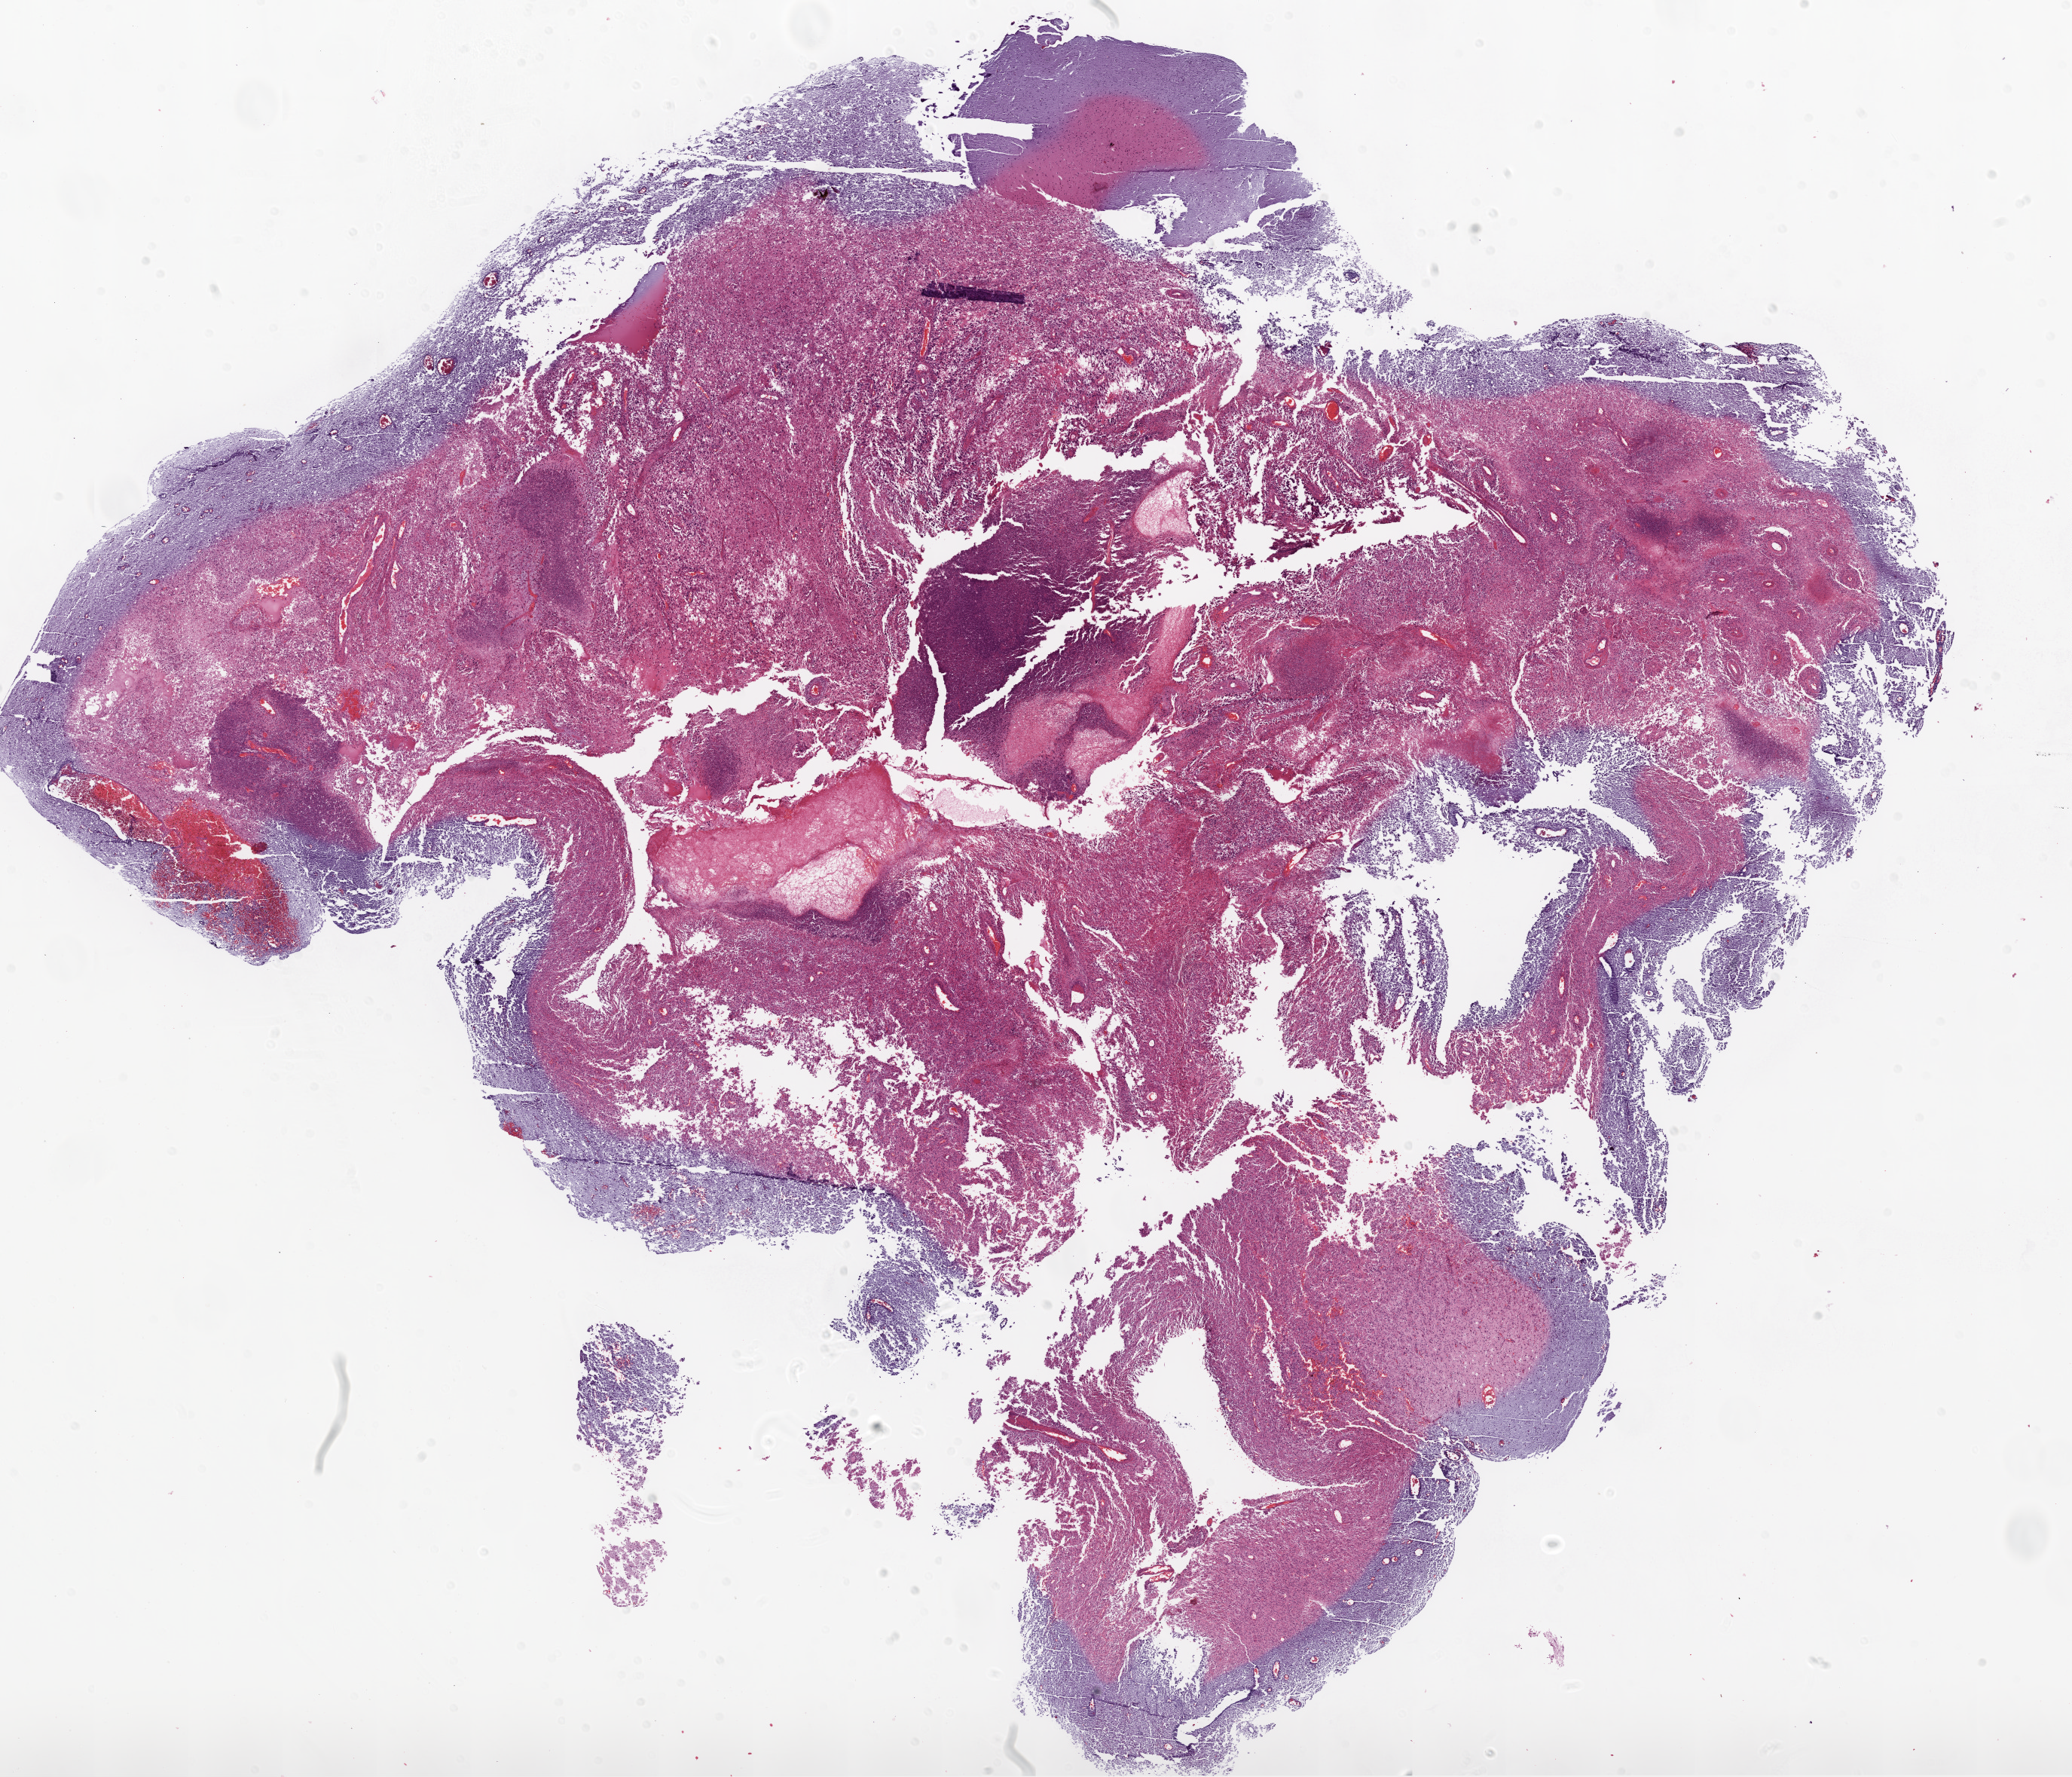
Whole-slide histology image, Hematoxylin and eosin (H&E) stained — shown as a low-resolution overview of the whole scanned area (about 22.1 x 18.9 mm), FFPE section, primary tumour sample from the brain. Male, age 61 years at initial diagnosis.
- histologic diagnosis: Glioblastoma